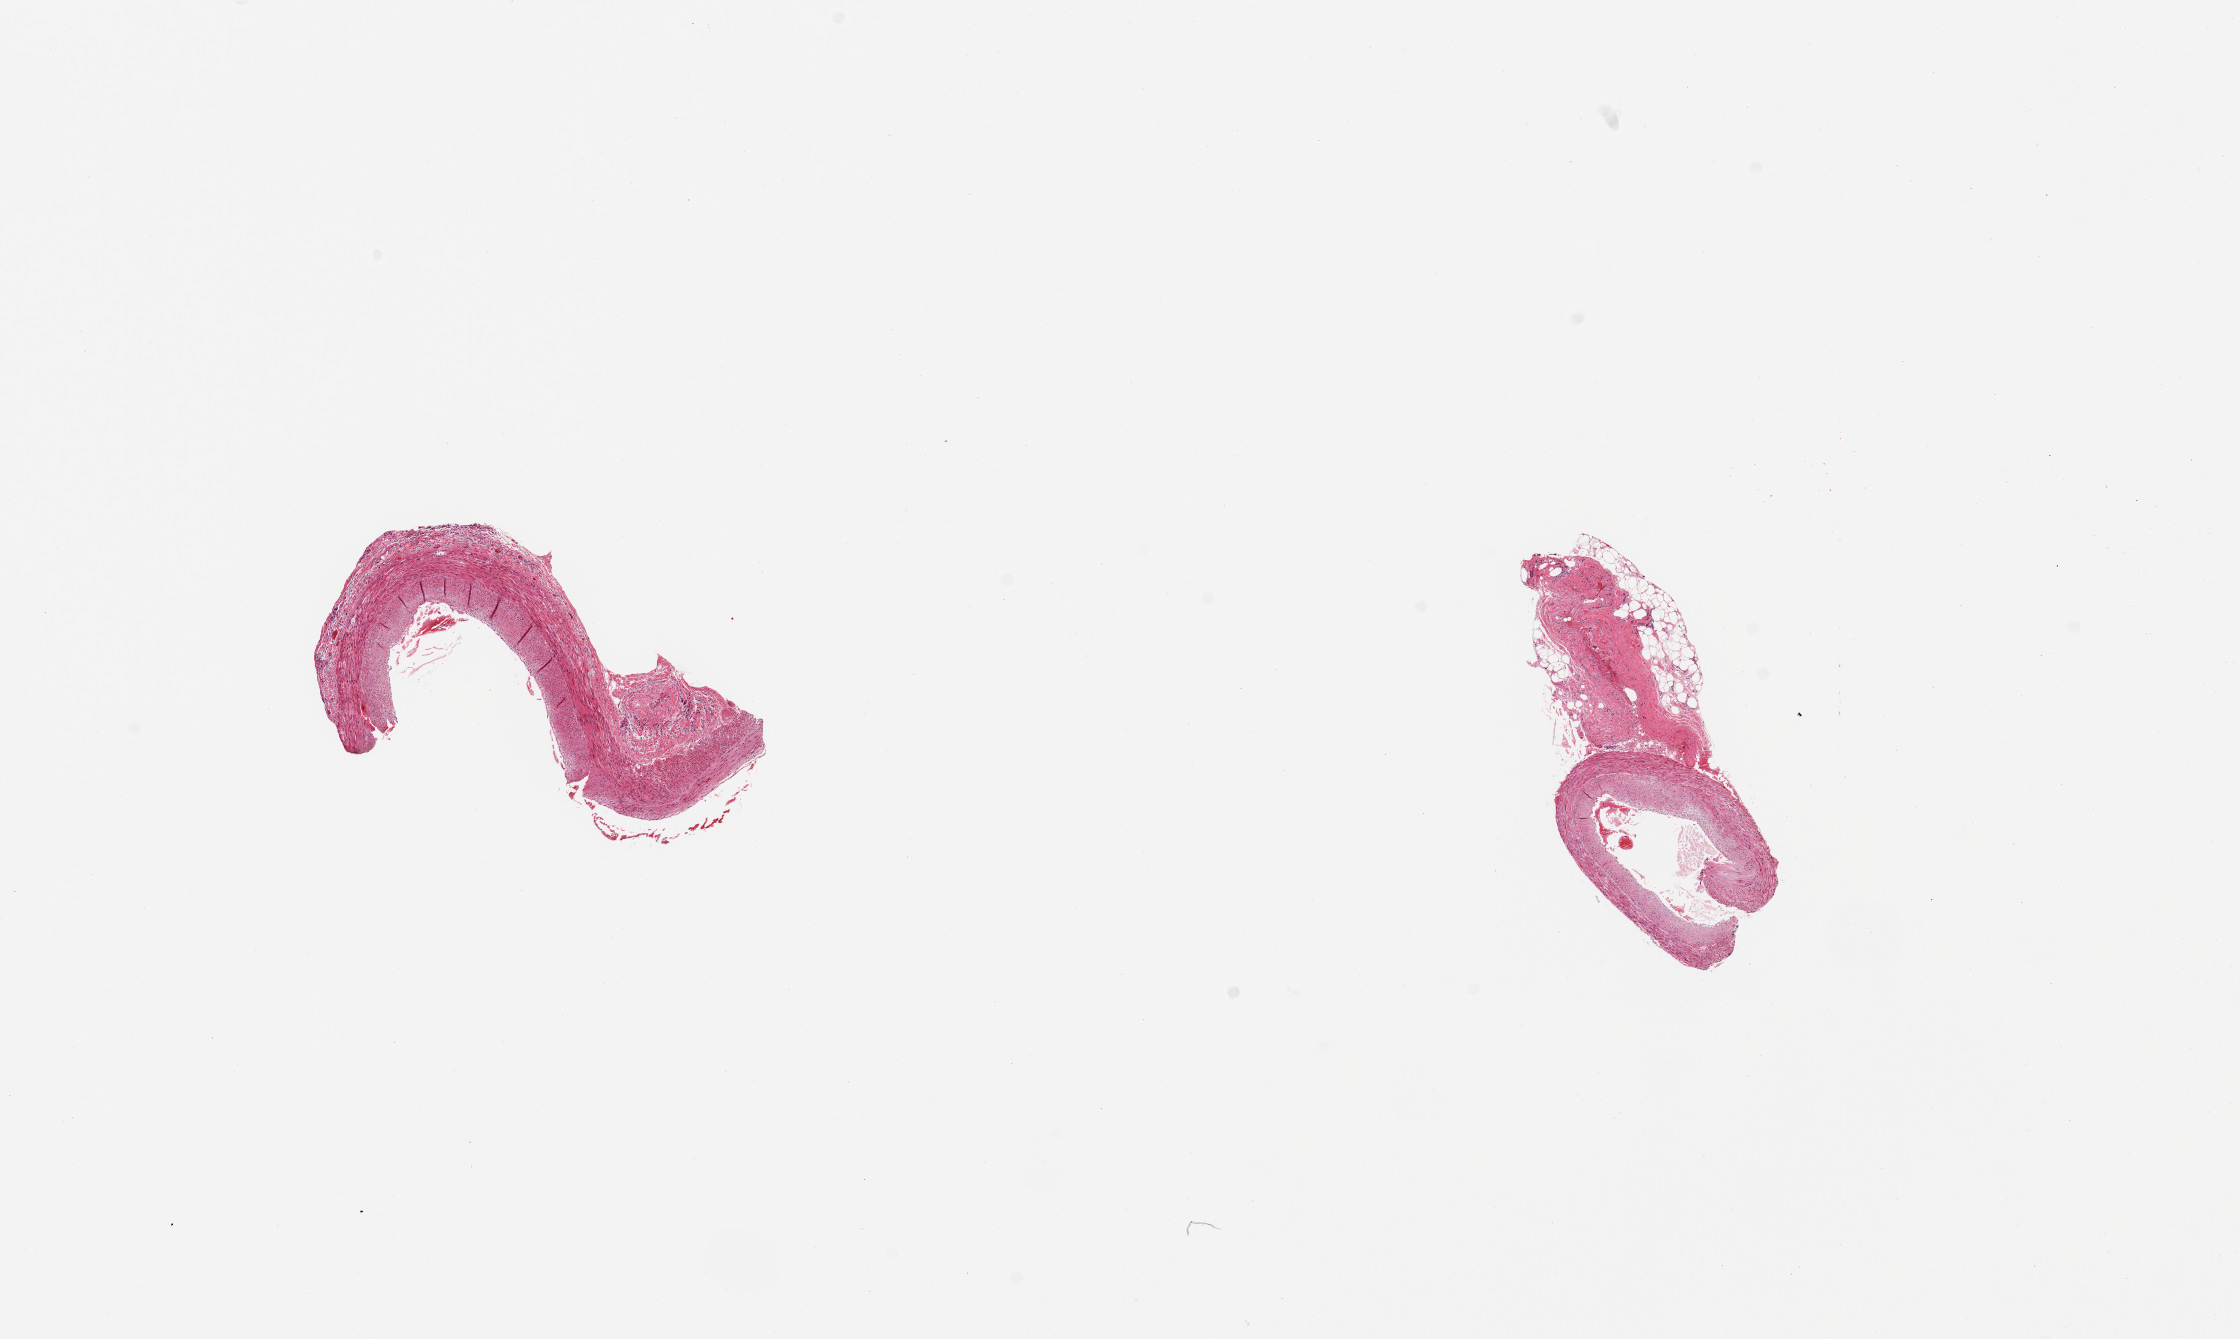
Whole-slide image, hematoxylin and eosin (H&E) stain, a low-resolution overview of the entire scanned area, about 17.7 x 10.6 mm (from a 20x scan). PAXgene-fixed paraffin-embedded (PFPE) section. Target tissue: coronary artery. Tissue donor sample. Donor sex: male.
Review note (as recorded): 2 pieces, fragmented, nubbin of adherent fat up to ~1.5mm on one section.